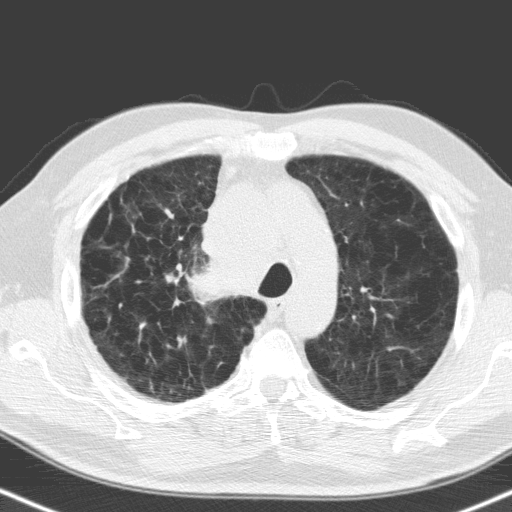
Low-dose screening chest CT, one axial slice; position 125 of 160 along the scan axis; 120 kVp; lung window (W 1500 / L -600 HU); 512 × 512 image matrix.
Outlined on this slice (outlined manually by an expert reader):
- lesion 1 (tumor, hilum of right lung): box from (x=189, y=256) to (x=242, y=301) px